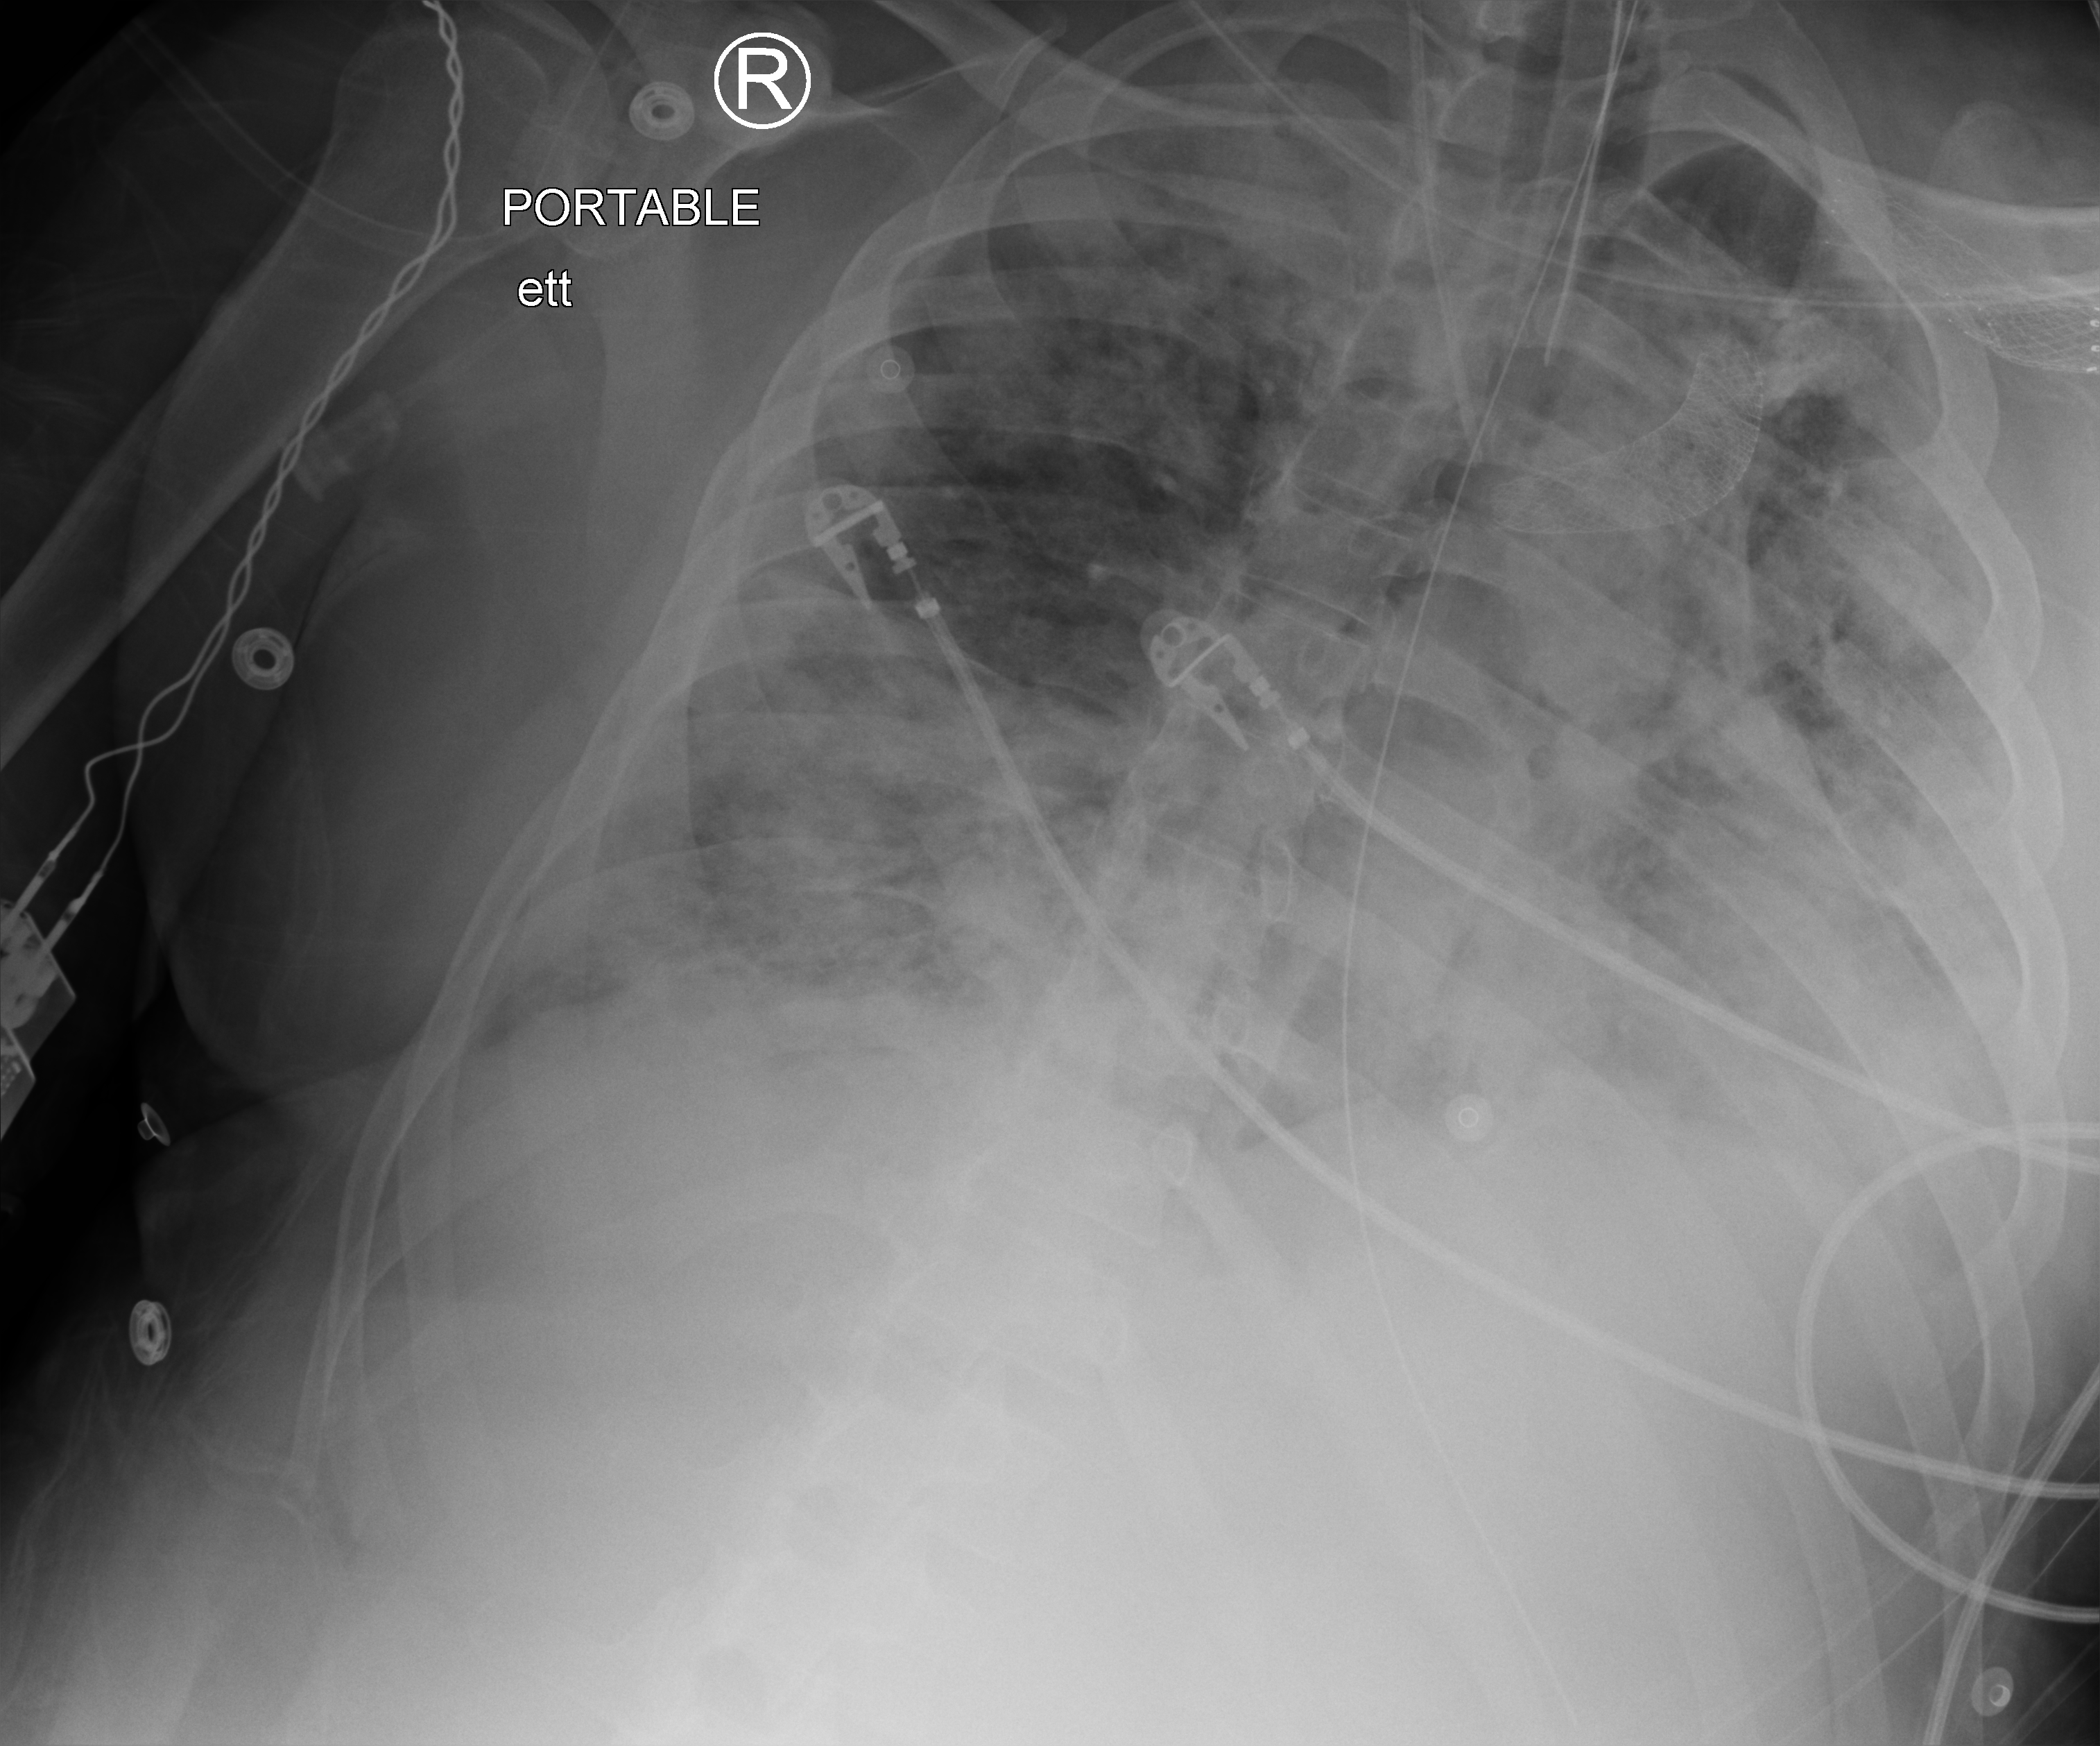
Bedside chest radiograph (computed radiography), anteroposterior (AP) projection. Patient hospitalised with COVID-19; male, aged 18–59 years.
Admission-level facts for this patient (not findings on this image; timing relative to this image not recorded): length of hospital stay: 41 days.